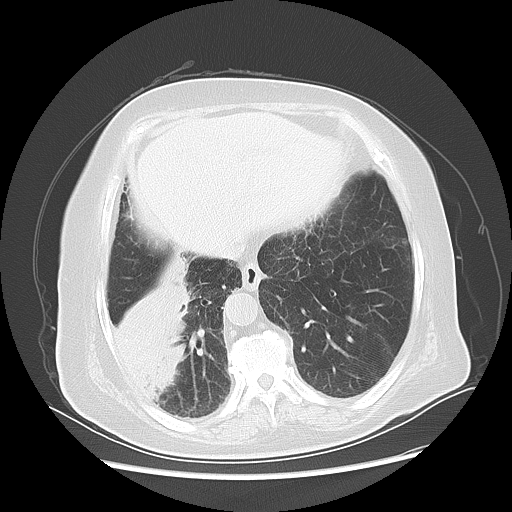
Chest CT, one axial slice; slice 16 of 56 in the series (ordered by position); 120 kVp; lung window (W 1500 / L -600 HU); 5 mm slice thickness; 512 × 512 image matrix, field of view 378 × 378 mm. Female patient, age 73 years. From the clinical record (not read from this slice): clinical TNM (as recorded): T3 N0 M0.
Structures marked on this image (rectangle marked by the reading radiologist):
- lung tumour (recorded histology: adenocarcinoma): bounding box <103,254,192,405> (left, top, right, bottom; pixels)